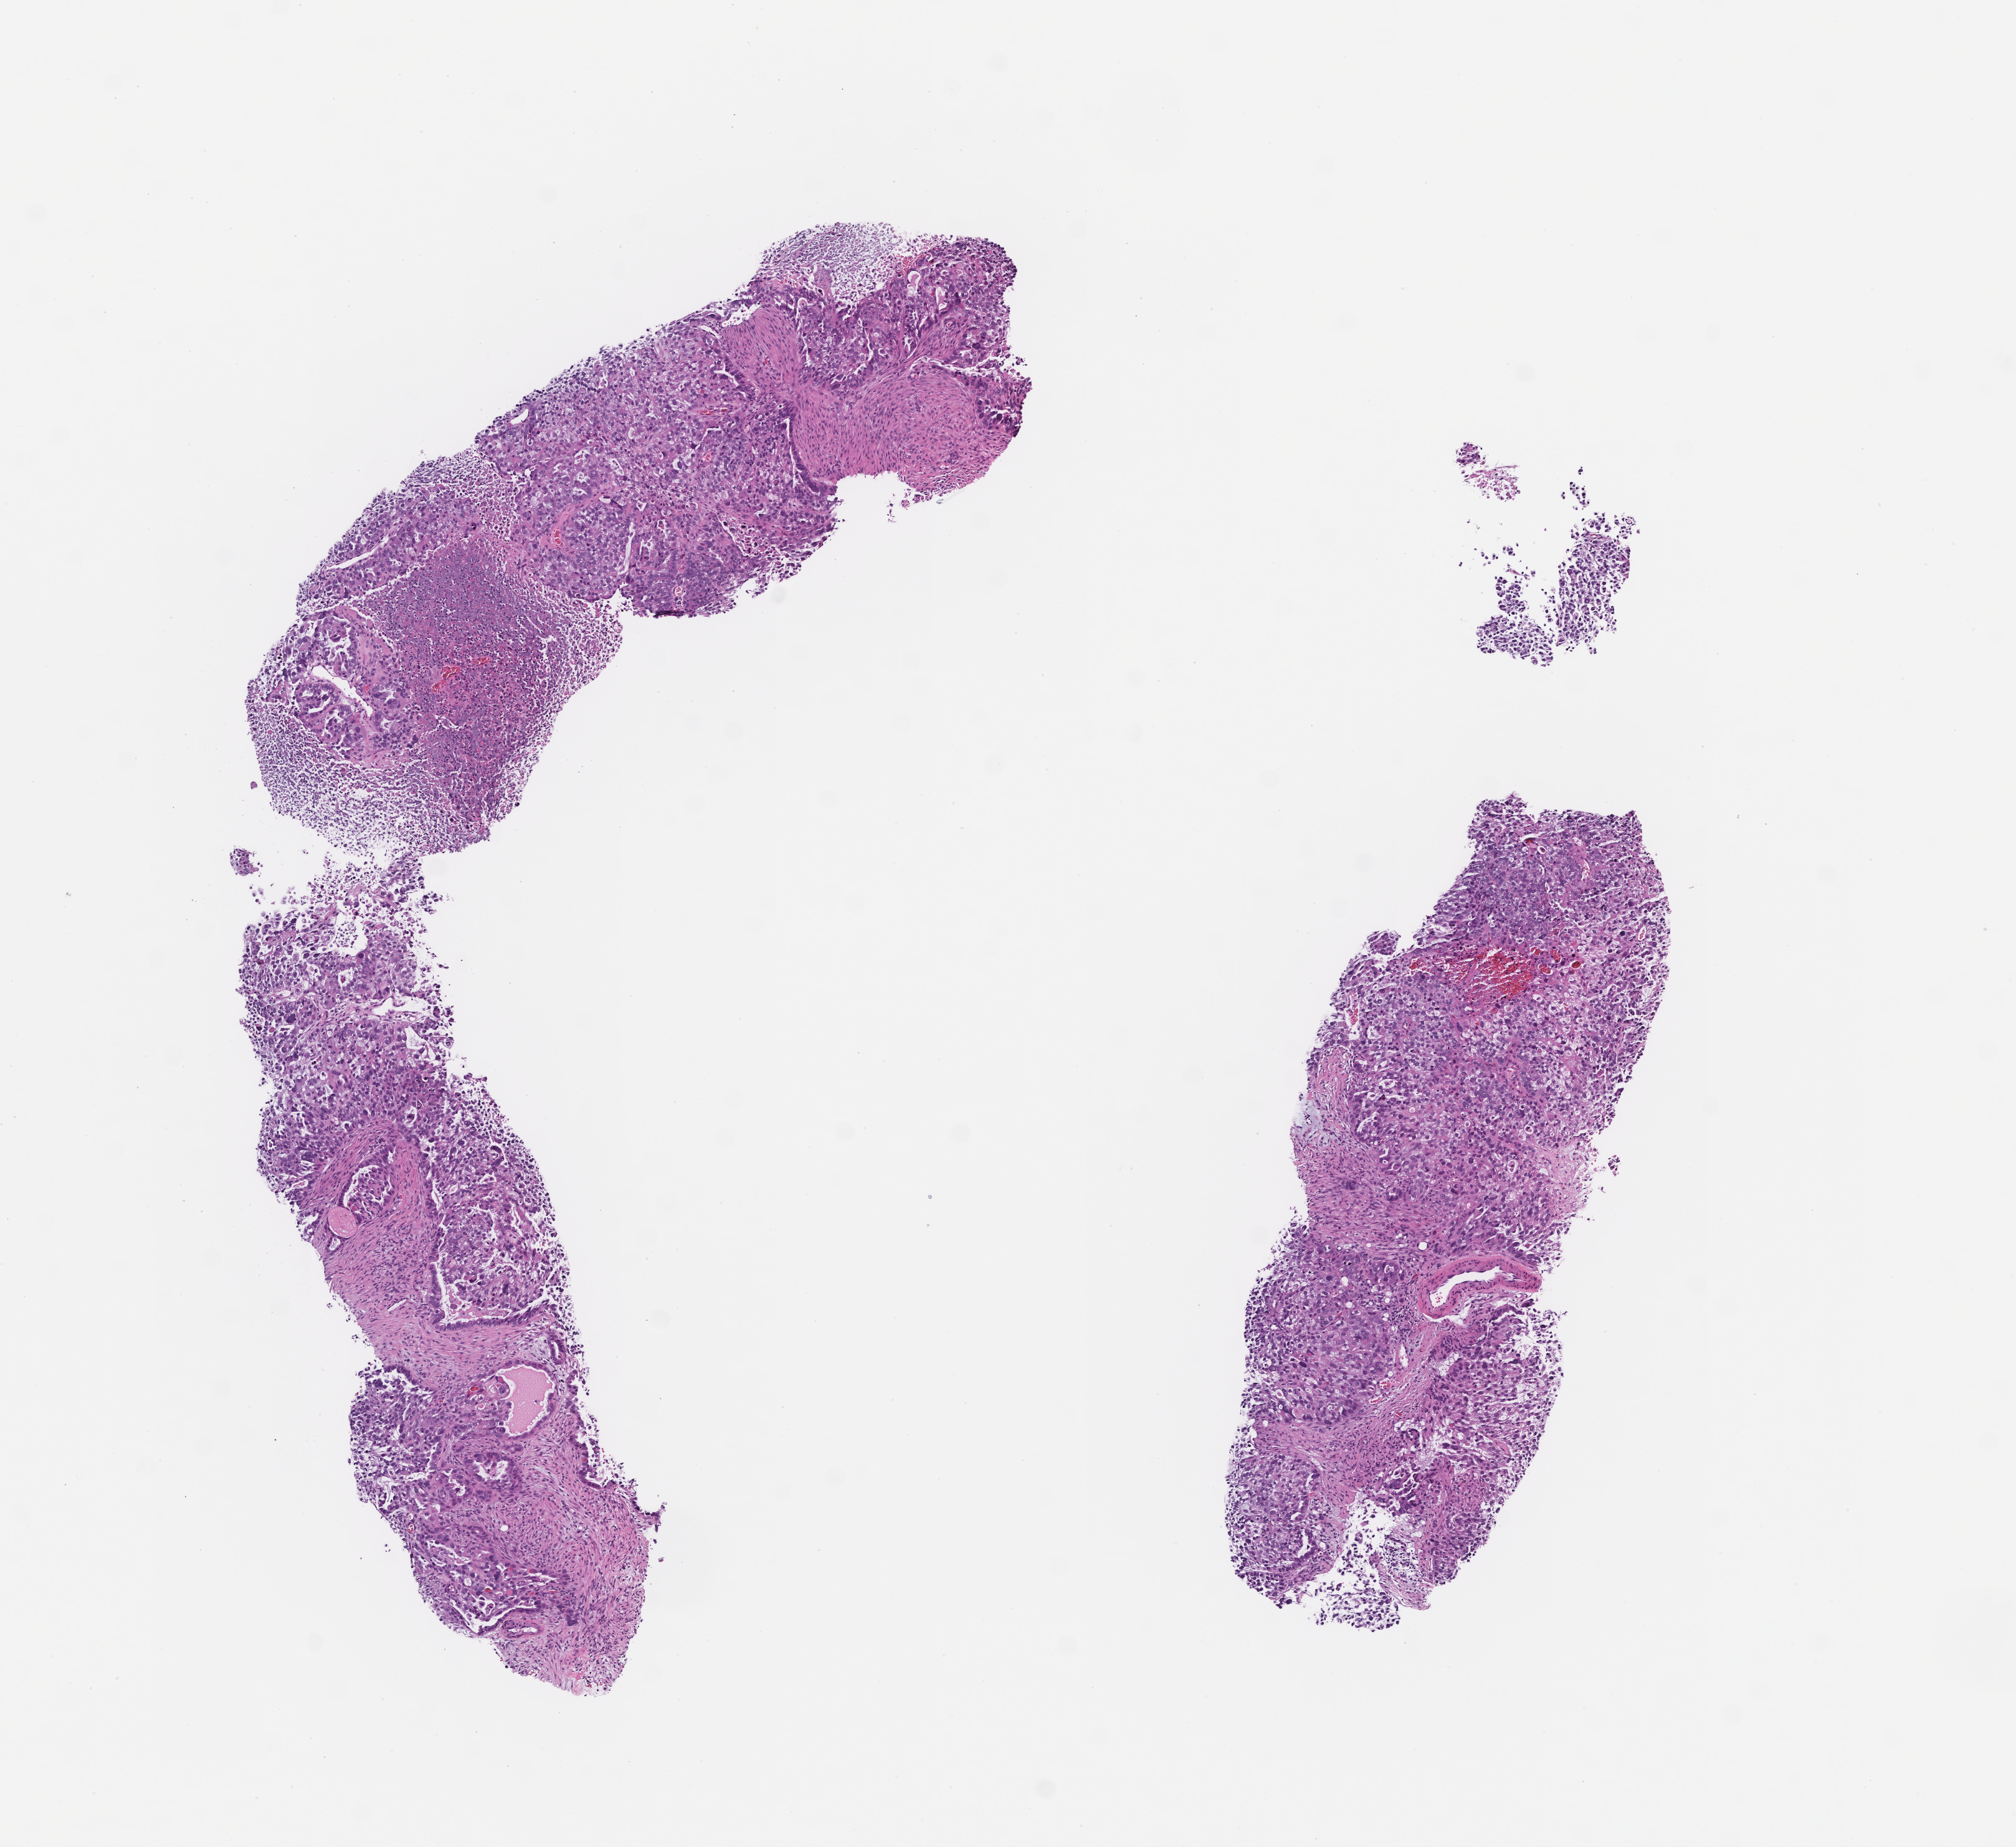
Digitized haematoxylin and eosin-stained section — a low-resolution overview of the entire scanned area, about 6.5 x 6.0 mm. Formalin-fixed paraffin-embedded section. Site: ovary. Patient: female.
* this section: primary tumor
* diagnosis: Ovarian Carcinoma